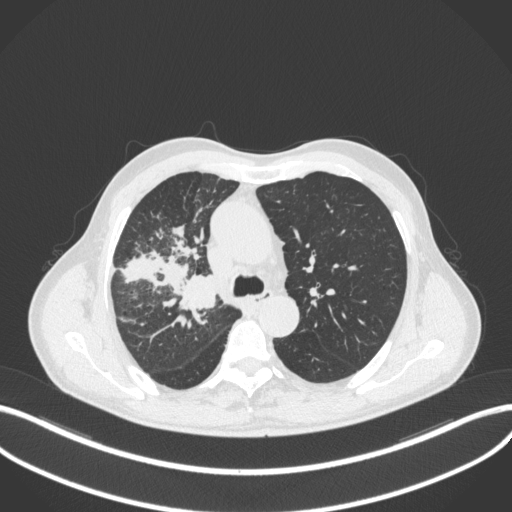
Chest CT, one axial slice. Position 331 of 490 along the scan axis. Reconstruction kernel B31f. 120 kVp. Lung window (W 1500 / L -600 HU). 1 mm slice thickness. 512 × 512 image matrix, field of view 400 × 400 mm. Male patient, age 69 years. From the clinical record (not read from this slice): clinical TNM (as recorded): T2a N0 M0.
Outlined on this slice (bounding box drawn by a radiologist):
- lung tumour (recorded histology: adenocarcinoma): box from (x=179, y=272) to (x=221, y=317) px